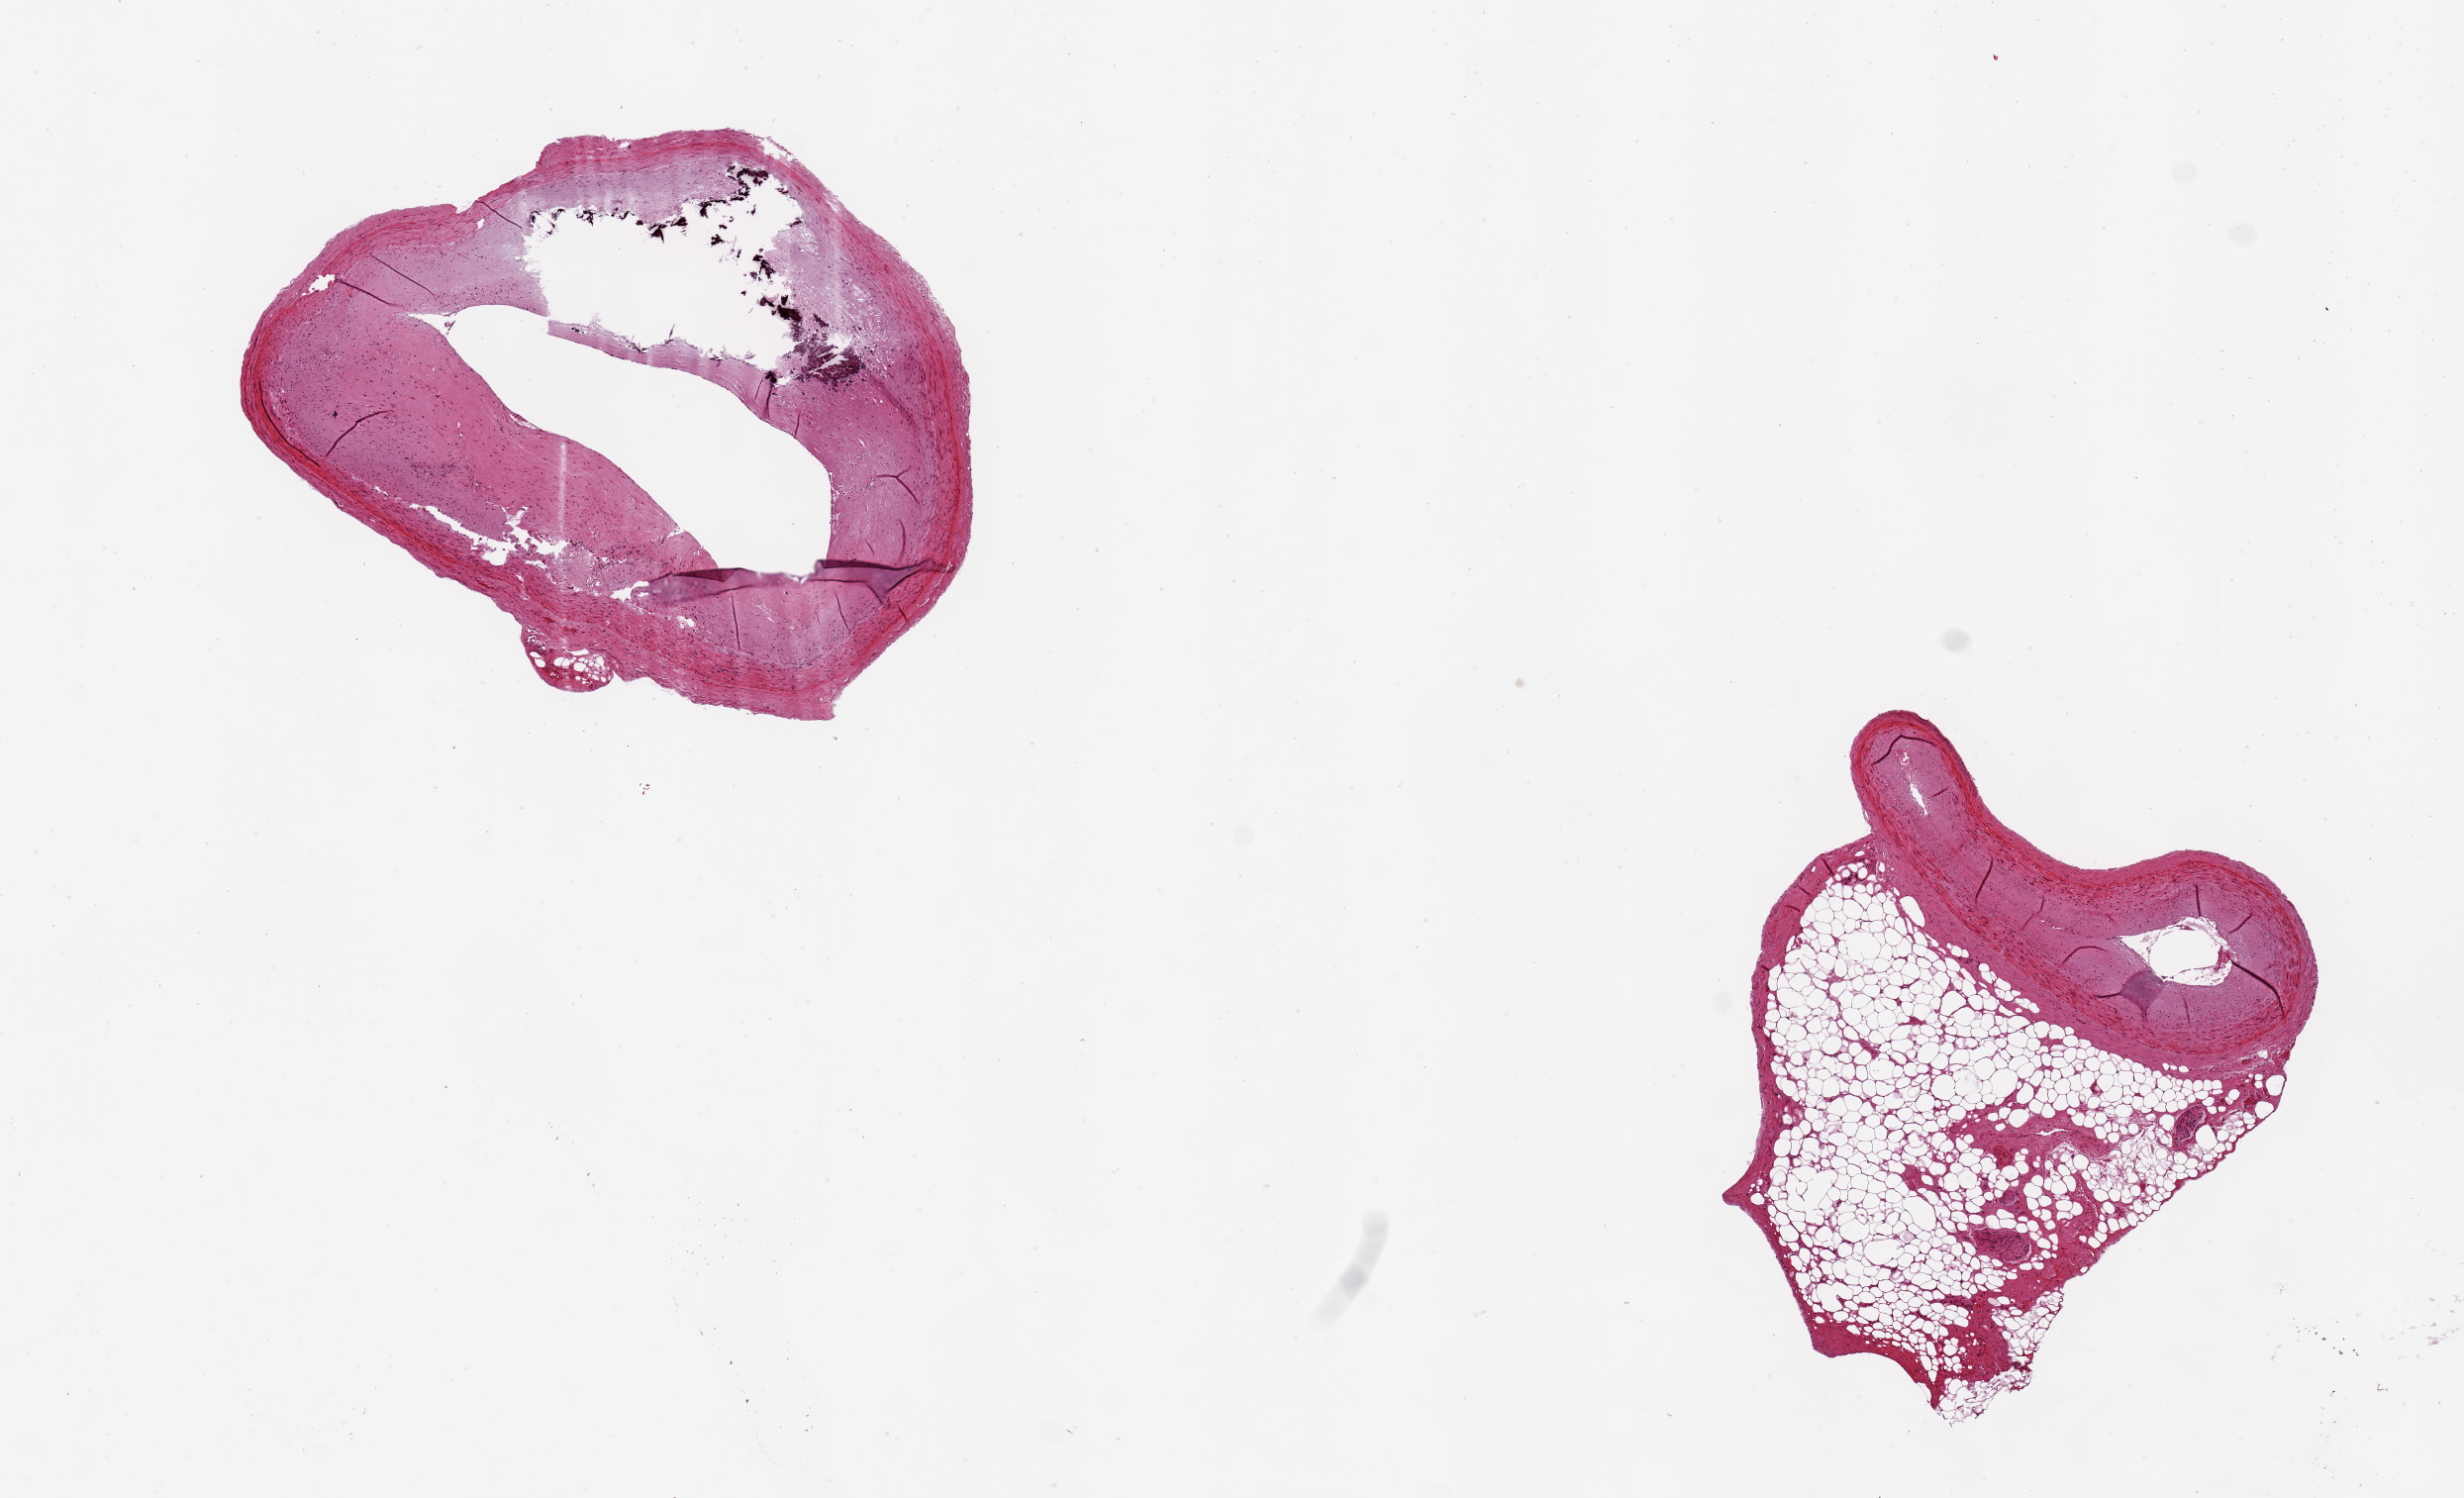
H&E whole-slide image — shown as a low-resolution overview of the whole scanned area (about 9.8 x 6.0 mm, from a 20x scan). PAXgene-fixed paraffin-embedded (PFPE) section. Sampled site (target tissue): coronary artery. Donor tissue sample.
Pathologist's review note for this sample: 2 pieces, subtotally occlusive calcified atherosclerosis, ~ 2mm d; One with 1.5mm ahderent fat nubbin.